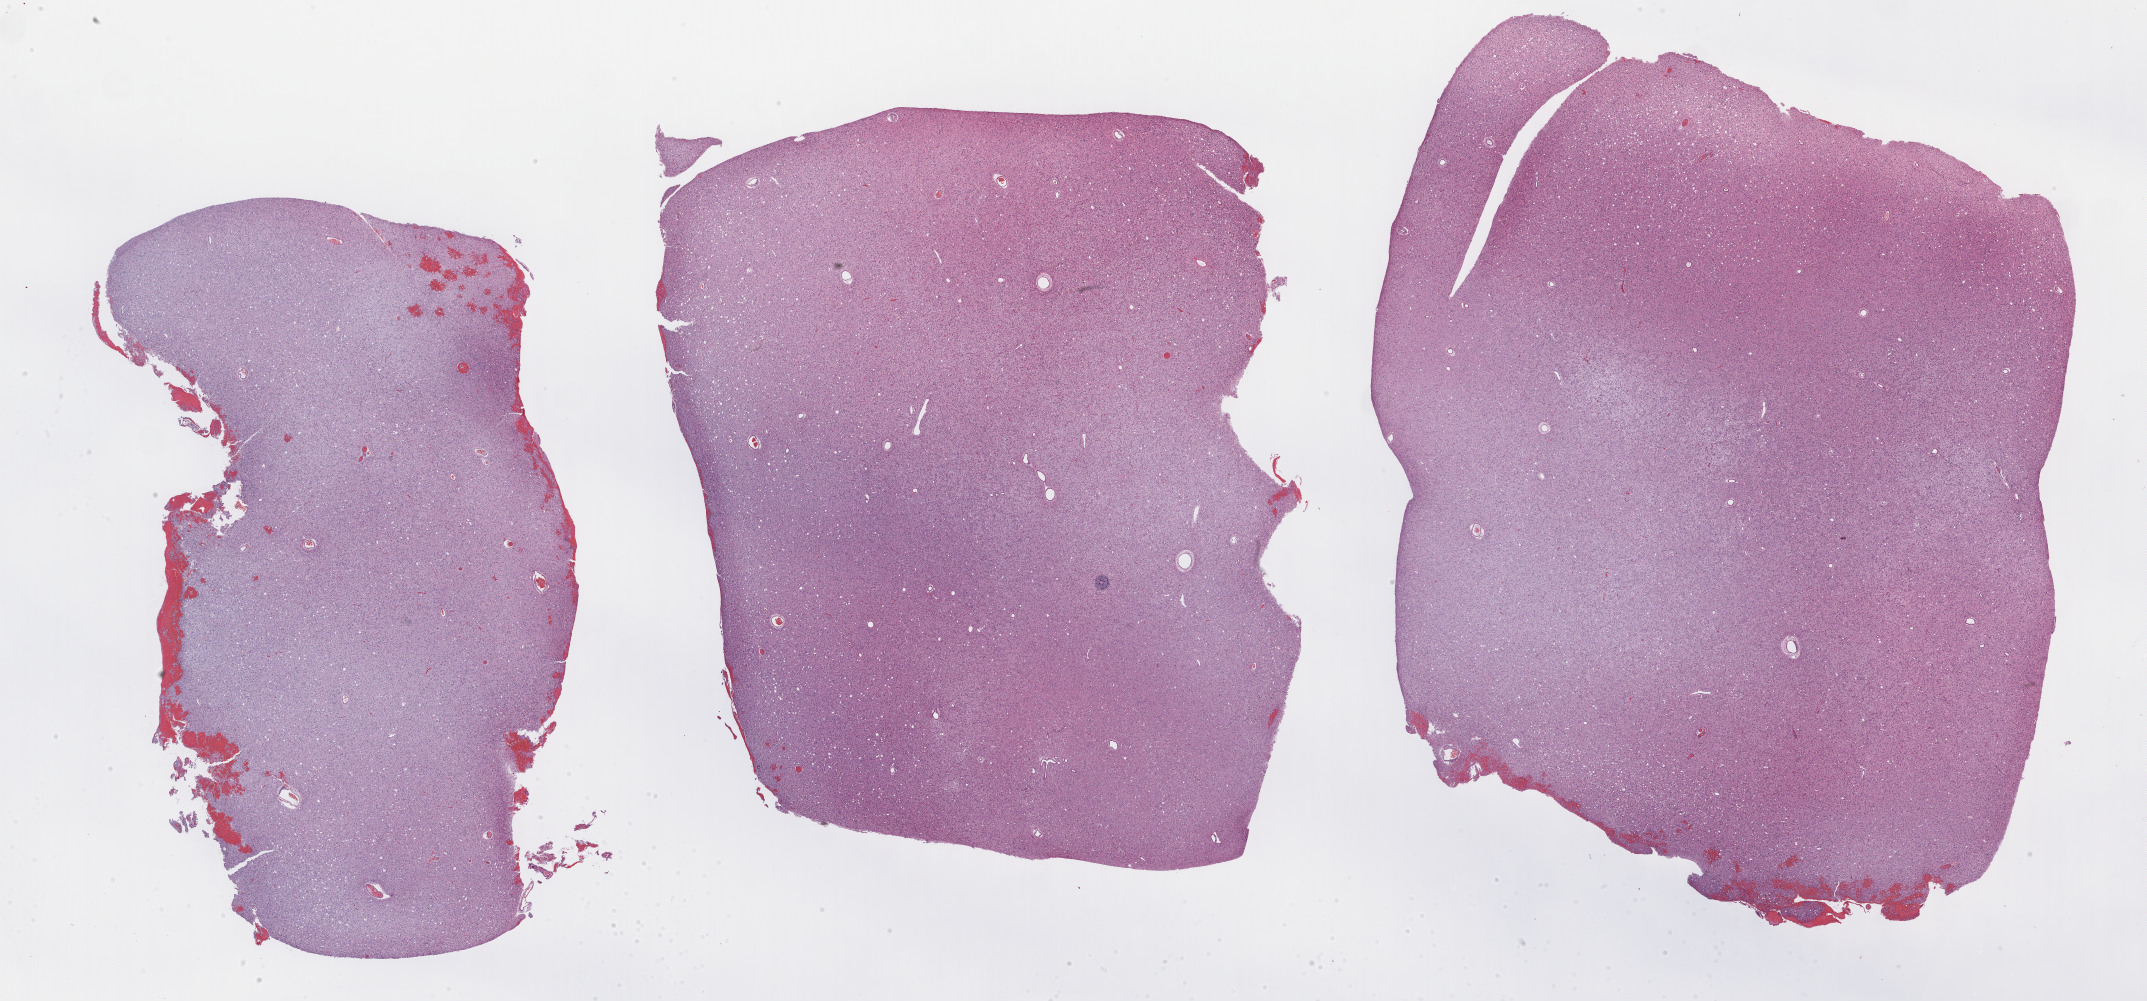
Whole-slide histology image, H&E-stained — whole scanned area (about 34.7 x 16.2 mm, from a 40x scan) shown as a low-resolution overview; FFPE section; brain, primary tumour sample. Patient: female, age at initial diagnosis 24 years. Histologic grade: G2 (moderately differentiated).
• pathologic diagnosis: Astrocytoma, NOS (cerebrum)